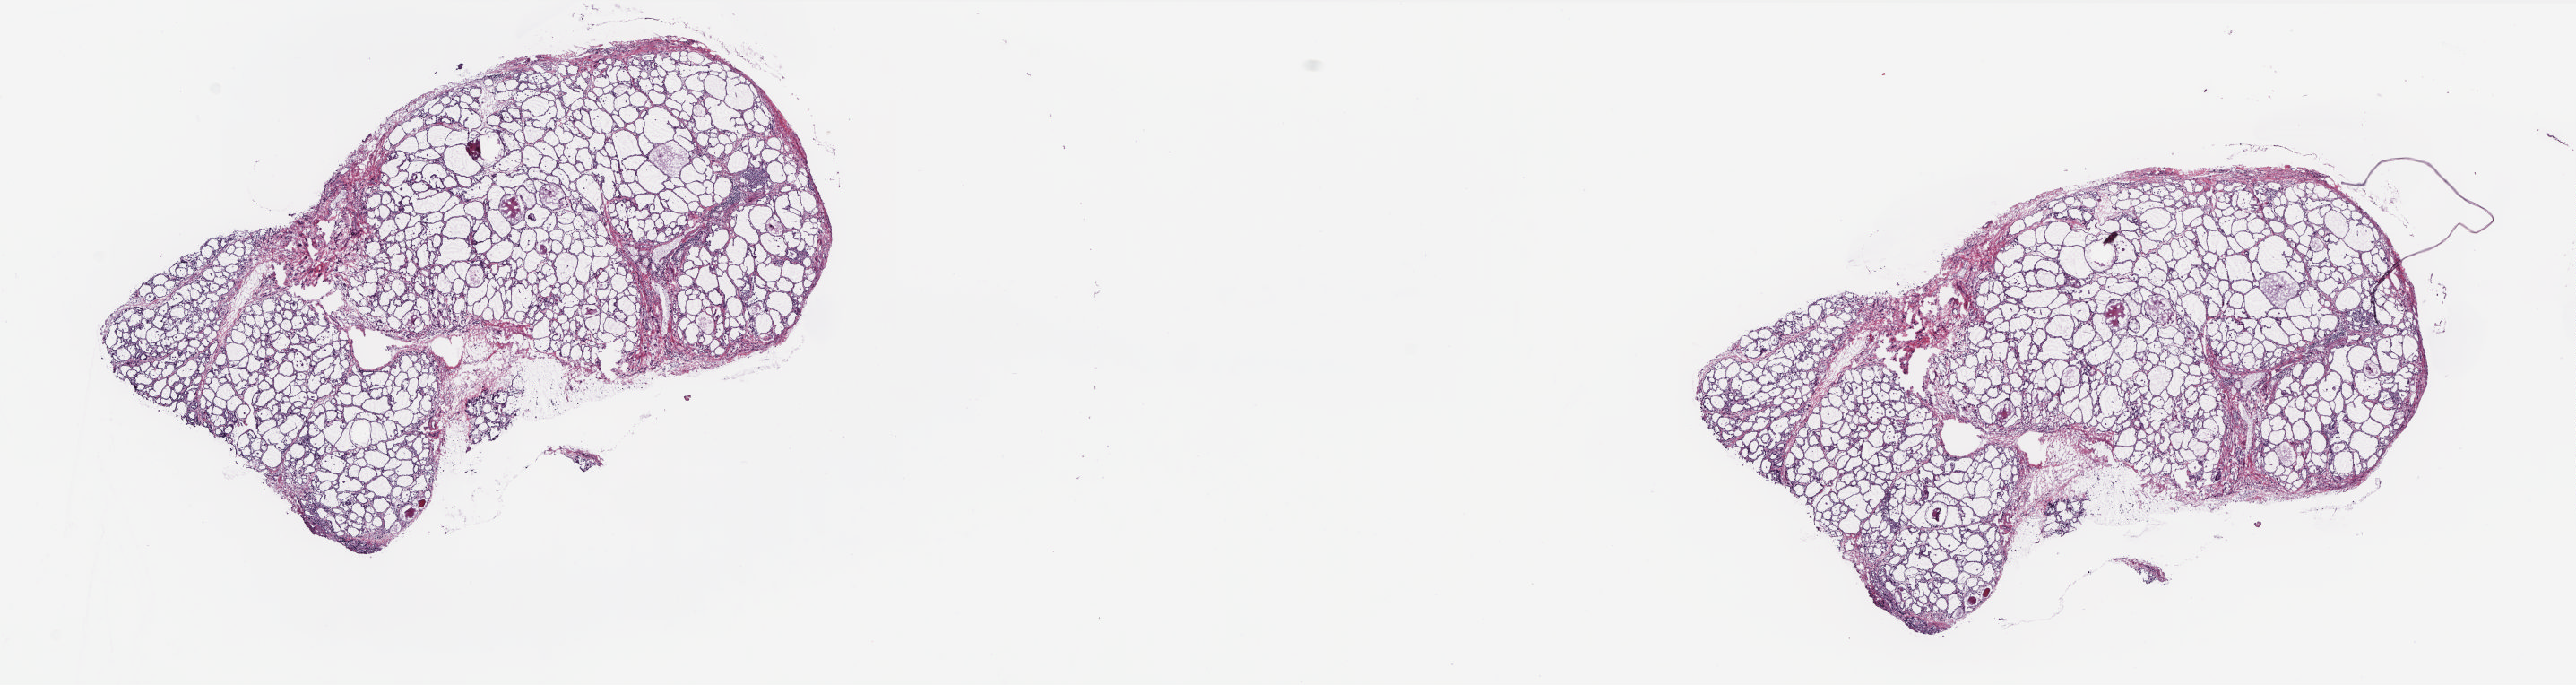
H&E-stained whole-slide image, a low-resolution overview of the entire scanned area, about 23.0 x 6.1 mm. Frozen section from the top of the tissue portion. Sample: solid tissue normal (non-tumour tissue), thyroid. Patient: female, age at initial diagnosis 29 years. Slide review estimates, as recorded: tumour cells 0%, tumour nuclei 0%, normal cells 90%, stromal cells 10%, necrosis 0%. Inflammatory infiltration, as recorded: lymphocyte infiltration 3%, monocyte infiltration 1%, neutrophil infiltration 1%.
• this section: solid tissue normal sample (biorepository sample class)
• patient diagnosis: Papillary adenocarcinoma, NOS (thyroid gland)